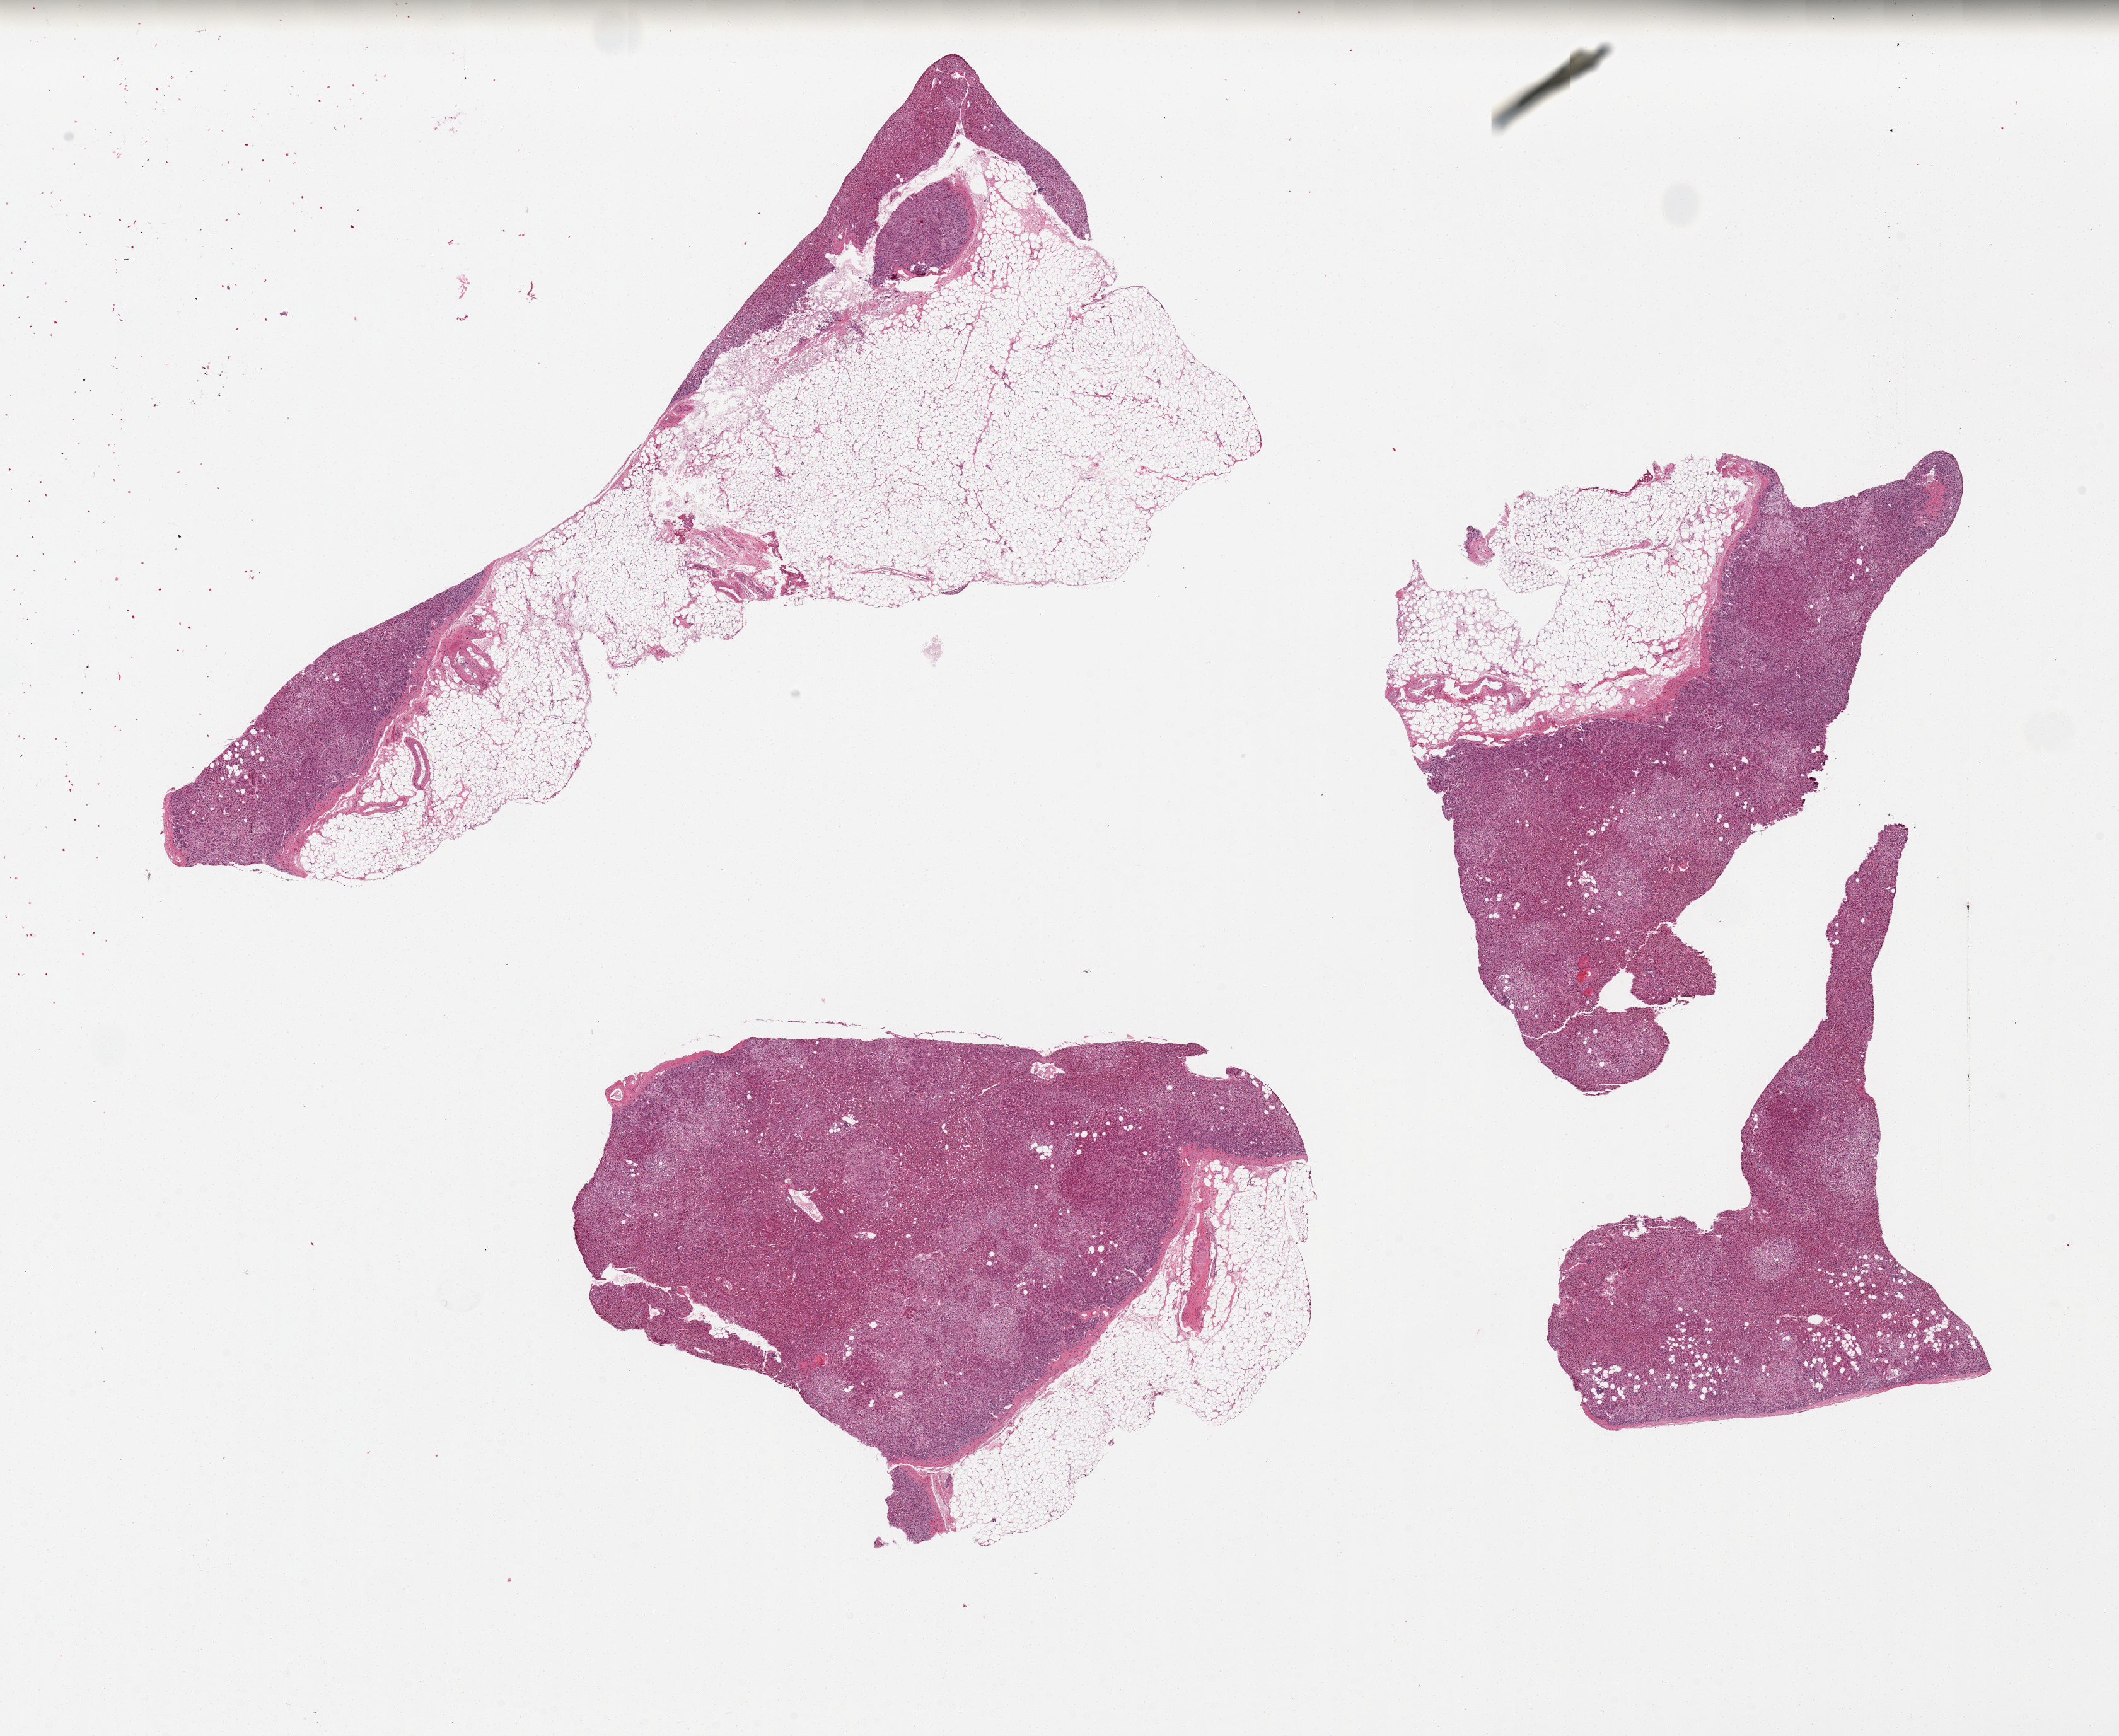
Digitized hematoxylin and eosin (H&E)-stained section, brightfield — shown as a low-resolution overview of the whole scanned area (about 26.6 x 21.8 mm, acquisition: 20x scan). PAXgene-fixed paraffin-embedded (PFPE) section. Target tissue: adrenal gland. Tissue donor sample. Male donor.
* review note (as recorded): 4 pieces; 3 with attached adipose tissue (up to 30% of submitted tissue)